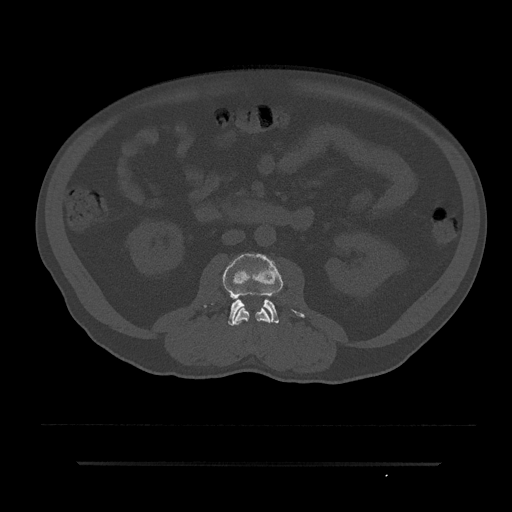
CT including the spine, one axial slice. Slice 32 of 797 in the series (ordered by position). Reconstruction kernel Br40s/3. Bone window (W 1800 / L 400 HU). 0.5 mm slice thickness. 512 × 512 image matrix. Patient: male, 59 years. From the clinical record (not read from this slice): primary cancer: bile ducts.
Structures marked on this image (semi-automatically segmented with operator editing):
- L2 vertebra: bounding box <233,302,272,342> (left, top, right, bottom; pixels)
- L3 vertebra: <223,254,304,325>